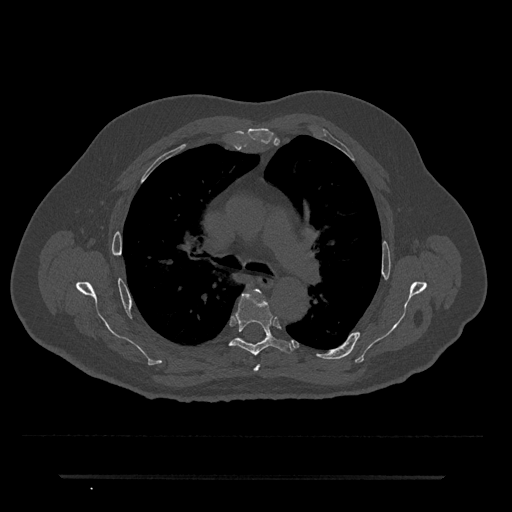
CT including the spine, one axial slice. Slice 486 of 797 in the series (ordered by position). Reconstruction kernel Br40s/3. Bone window (W 1800 / L 400 HU). 0.5 mm slice thickness. 512 × 512 image matrix. Patient: male, 69 years. Case-level facts recorded for this patient, not image findings: primary cancer: prostate.
Outlined on this slice (semi-automatic segmentation, software-assisted and operator-edited):
- T4 vertebra: bounding box <253,289,261,372> (left, top, right, bottom; pixels)
- T5 vertebra: <230,290,293,355>